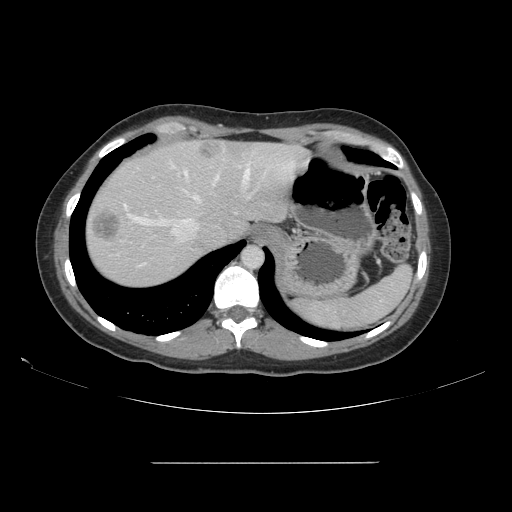
Contrast-enhanced abdominal CT, one axial slice; slice 126 of 151 in the series (ordered by position); 120 kVp; intravenous contrast given; soft-tissue window (W 400 / L 40 HU); 2.5 mm slice thickness; 512 × 512 image matrix, field of view 421 × 421 mm. Female patient, age 46 years. From the clinical record (not read from this slice): diagnosis: colorectal cancer liver metastases, imaged before liver resection; multiple liver metastases: yes.
Structures marked on this image (outlined manually by an expert reader):
- hepatic veins: box from (x=124, y=152) to (x=256, y=241) px
- liver: (x=86, y=140)–(x=303, y=288)
- planned liver remnant (the part of the liver to remain after resection): (x=97, y=143)–(x=303, y=243)
- liver metastasis: (x=93, y=213)–(x=121, y=243)
- liver metastasis: (x=200, y=144)–(x=224, y=160)